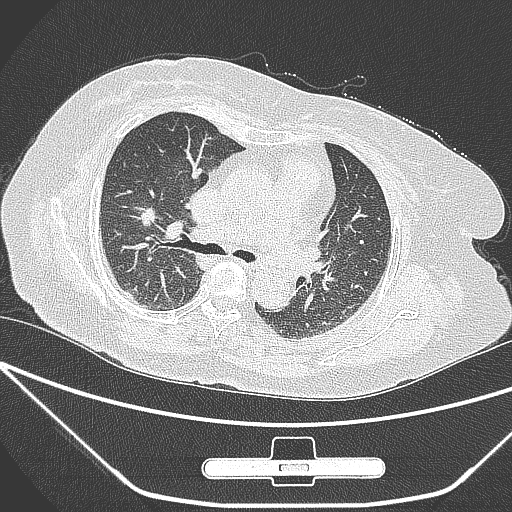
Chest CT, one axial slice; 120 kVp; lung window (W 1500 / L -600 HU); 1 mm slice thickness; 512 × 512 image matrix. Female patient, age 65 years. From the clinical record (not read from this slice): clinical TNM (as recorded): T1c N0 M0.
Outlined on this slice (rectangle marked by the reading radiologist):
- lung tumour (recorded histology: adenocarcinoma): bounding box [x1, y1, x2, y2] px = [136, 198, 166, 251]